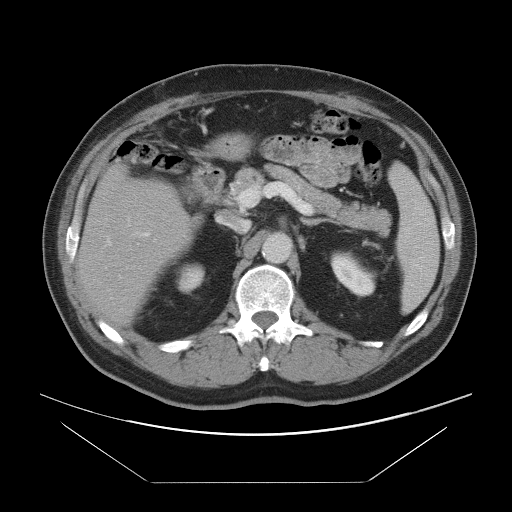
Contrast-enhanced abdominal CT, one axial slice. Slice 49 of 97 in the series (ordered by position). Intravenous contrast given. Soft-tissue window (W 400 / L 40 HU). 512 × 512 image matrix. Male patient, age 62 years. From the clinical record (not read from this slice): diagnosis: colorectal cancer liver metastases, imaged before liver resection; multiple liver metastases: no; largest metastasis: 7 cm; disease in both lobes: yes.
Outlined on this slice (outlined manually by an expert reader):
- hepatic veins: bounding box (x1, y1, x2, y2) in pixels: (105, 218, 130, 246)
- liver: (79, 168, 189, 323)
- planned liver remnant (the part of the liver to remain after resection): (79, 174, 189, 322)
- portal vein (with intrahepatic branches): (140, 232, 150, 236)